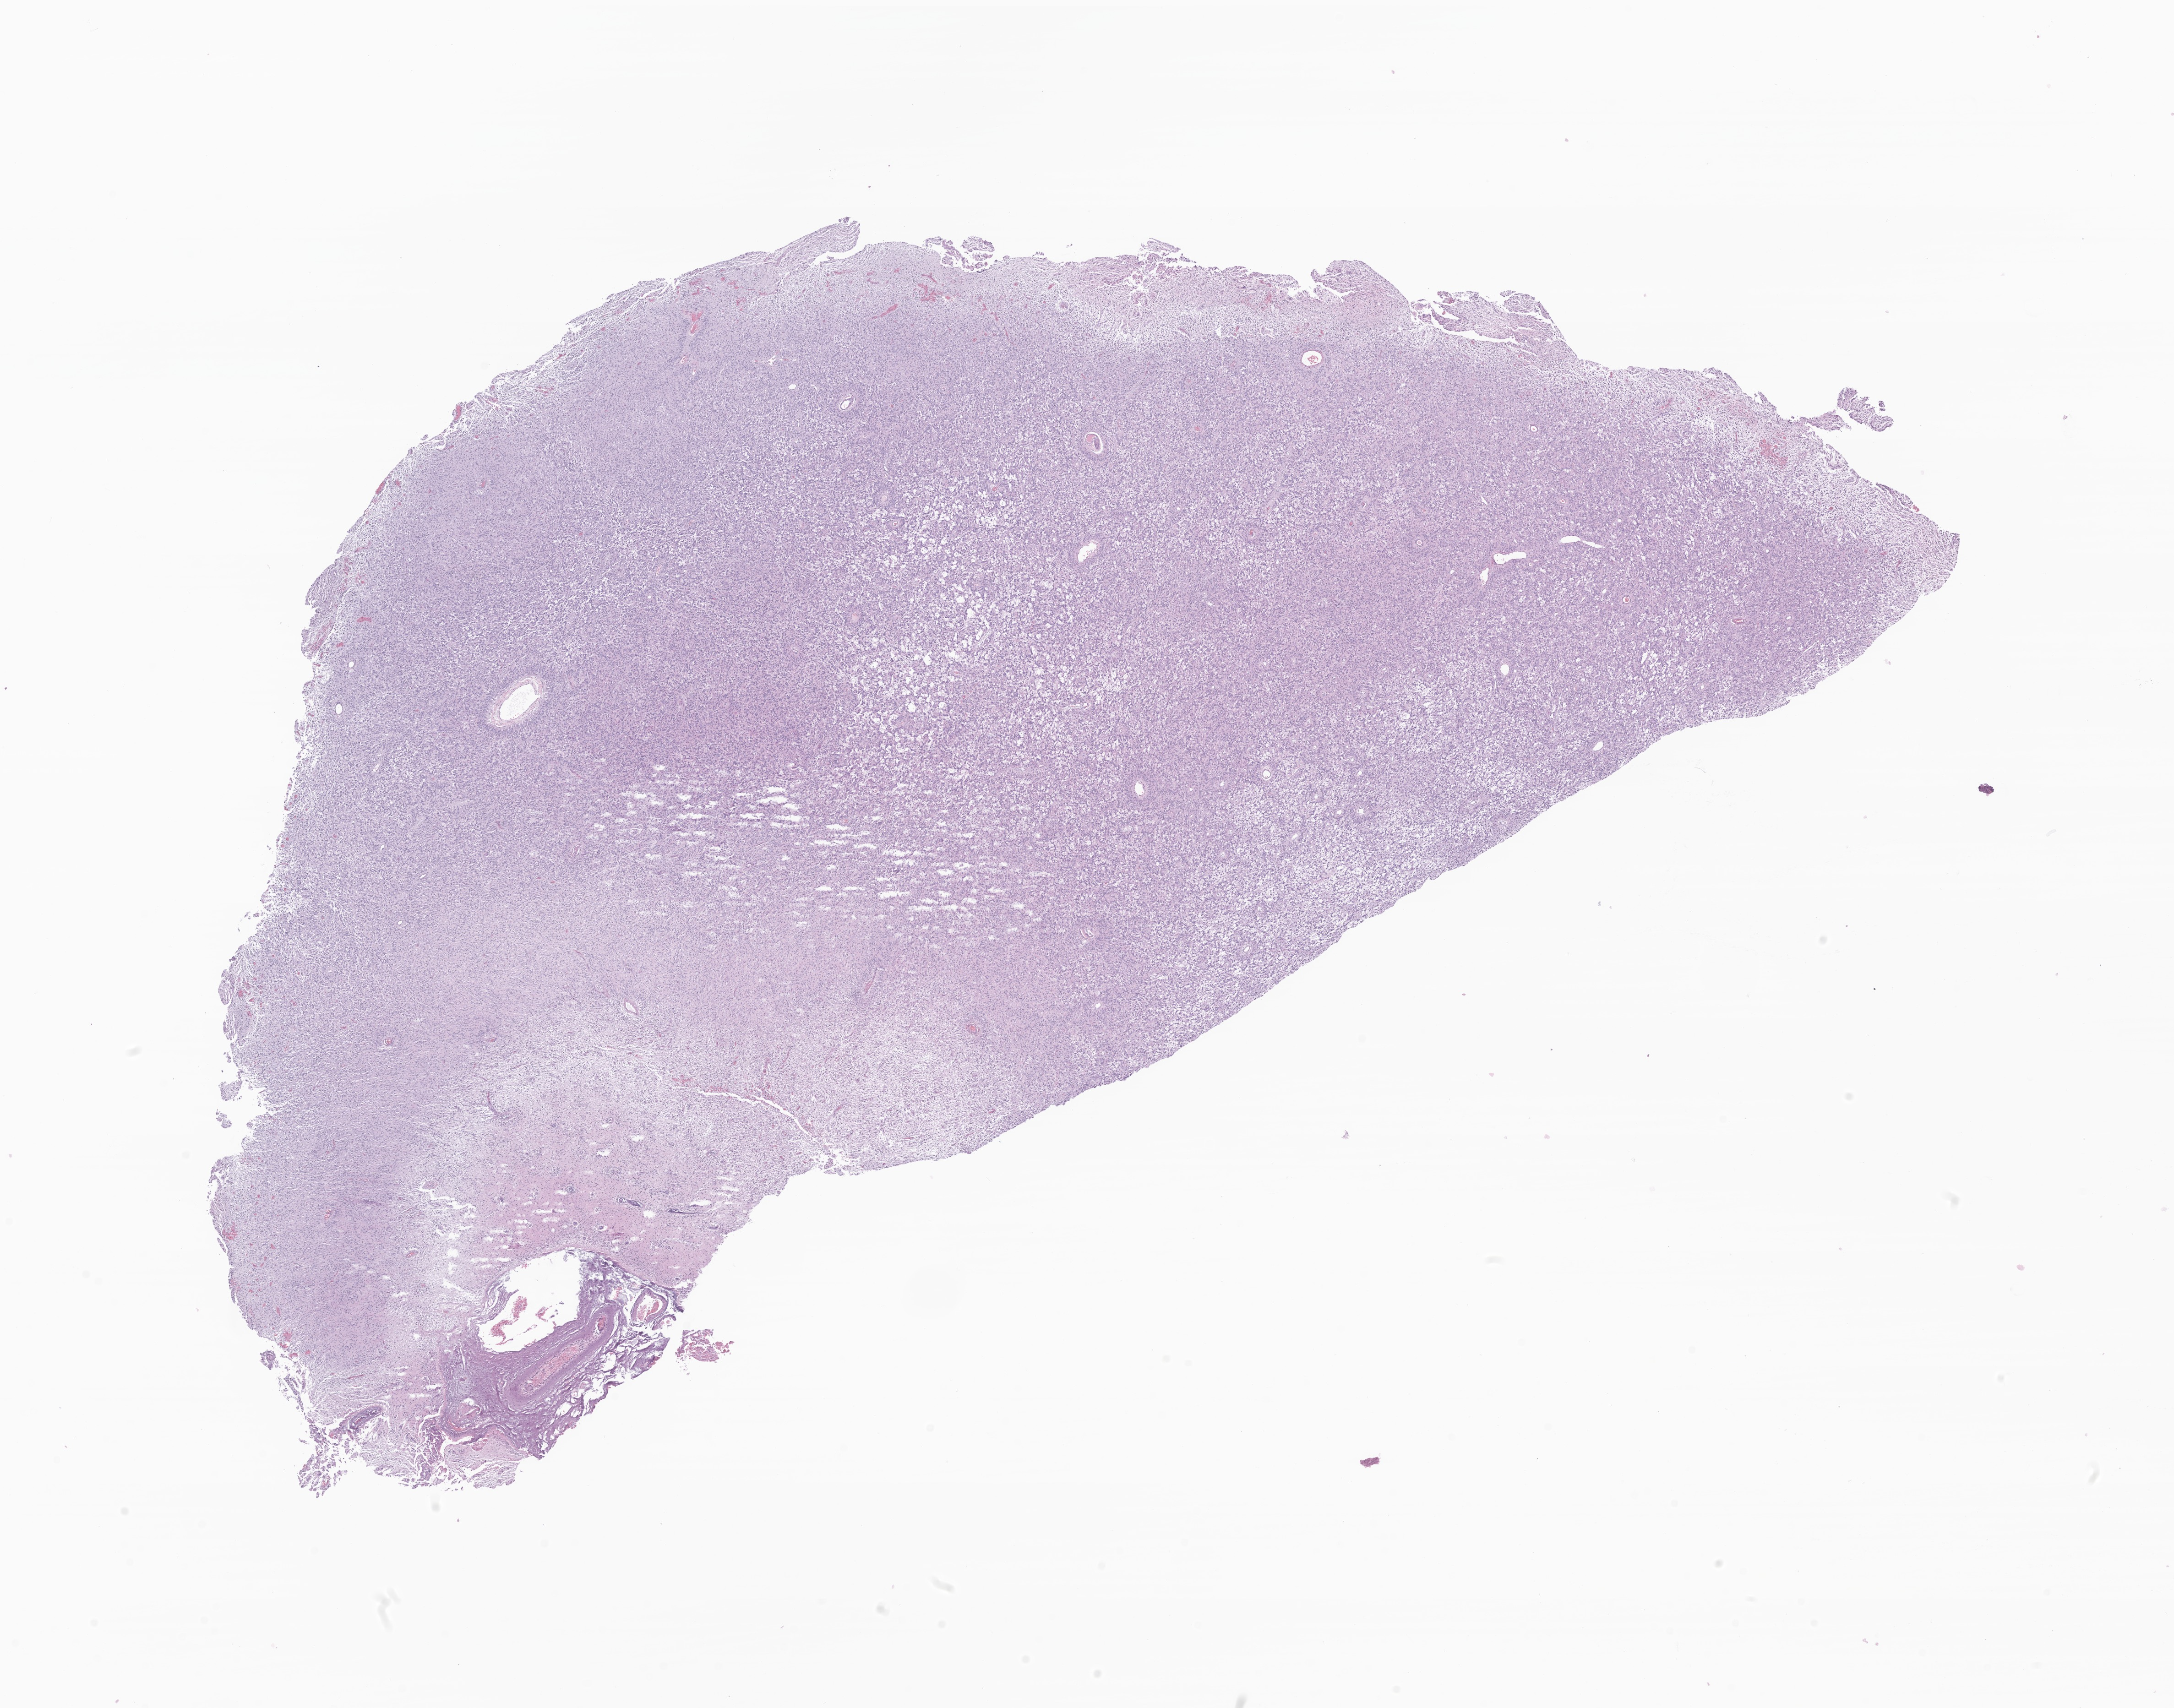
Digitized H&E-stained section of tumor tissue from the brain, a low-resolution overview of the entire scanned area, about 20.0 x 15.7 mm; FFPE section. Male patient, age 109 months (9 years 1 month).
Diagnosis: Neoplasm, uncertain whether benign or malignant.